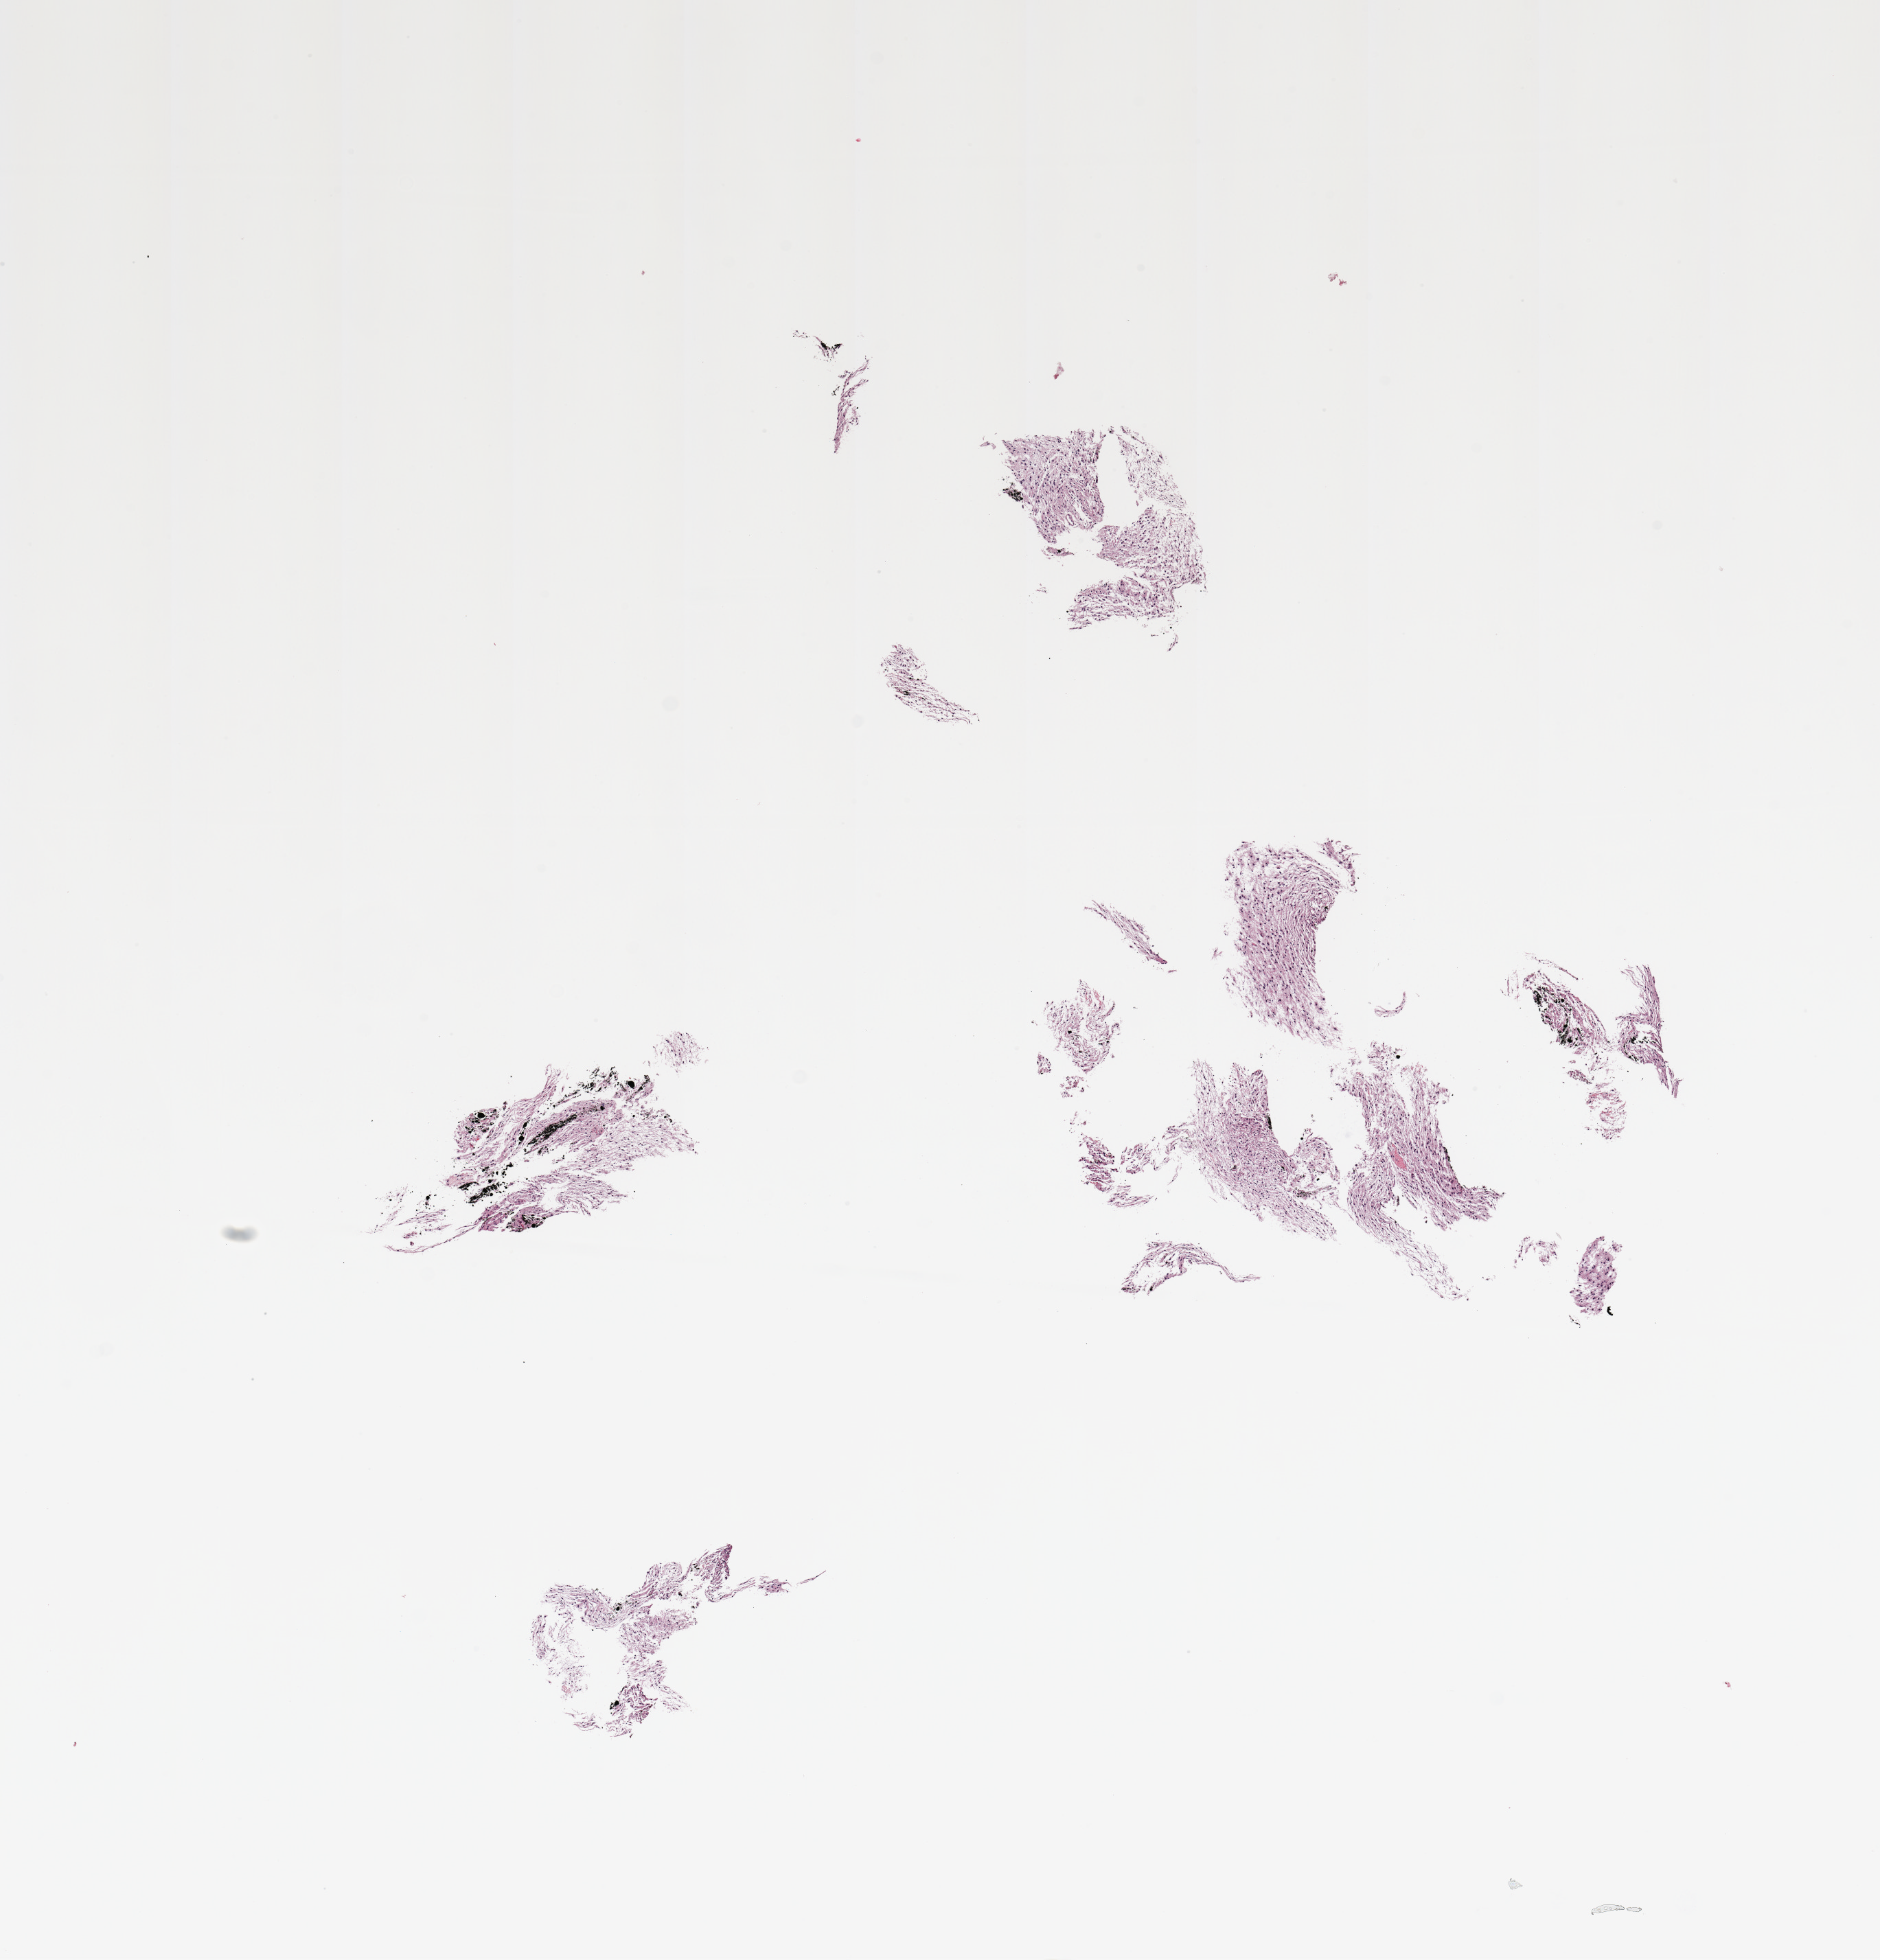
H&E whole-slide image, shown as a low-resolution overview of the whole scanned area (about 10.8 x 11.3 mm, slide scanned at 20x). Tumour tissue sample, sampled site: frontal lobe. Patient: male, age 34 years.
Diagnosis: Glioblastoma.